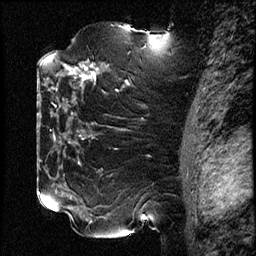
Breast MRI (dynamic contrast-enhanced), one sagittal slice. Slice 50 of 78 in the series (ordered by position). Dynamic contrast-enhanced study with each time point stored as its own series, time point 2 of 3 at this slice position (early post-contrast, ordered by acquisition time). 1.5 T. TE 4.2 ms, TR 17.6 ms. 2 mm slice thickness. 256 × 256 image matrix, field of view 200 × 200 mm. Female patient, age 42 years. Case-level facts recorded for this patient, not image findings: setting: breast cancer imaged before/during neoadjuvant chemotherapy; receptor status: HER2-positive.
Outlined on this slice (semi-automatic segmentation, software-assisted and operator-edited):
- analysis volume of interest (the breast-tissue region the enhancement analysis was run in; not a lesion): bounding box [x1, y1, x2, y2] px = [50, 51, 131, 129]
- tumour enhancement mask (voxels above the 100 % enhancement threshold inside the analysis volume of interest): [64, 65, 99, 81]